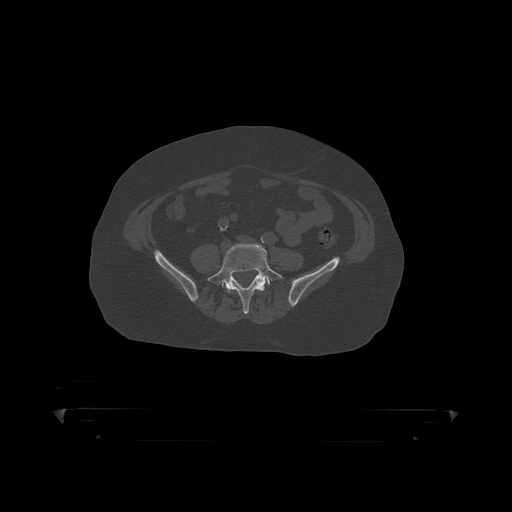
CT including the spine, one axial slice; slice 42 of 390 in the series (ordered by position); reconstruction kernel STANDARD; 120 kVp; bone window (W 1800 / L 400 HU); 1.25 mm slice thickness; 512 × 512 image matrix, field of view 650 × 650 mm. Patient: male, 60 years. From the clinical record (not read from this slice): primary cancer: prostate.
Structures marked on this image (semi-automatic segmentation, software-assisted and operator-edited):
- L4 vertebra: bounding box <228,285,265,294> (left, top, right, bottom; pixels)
- L5 vertebra: <208,243,283,314>